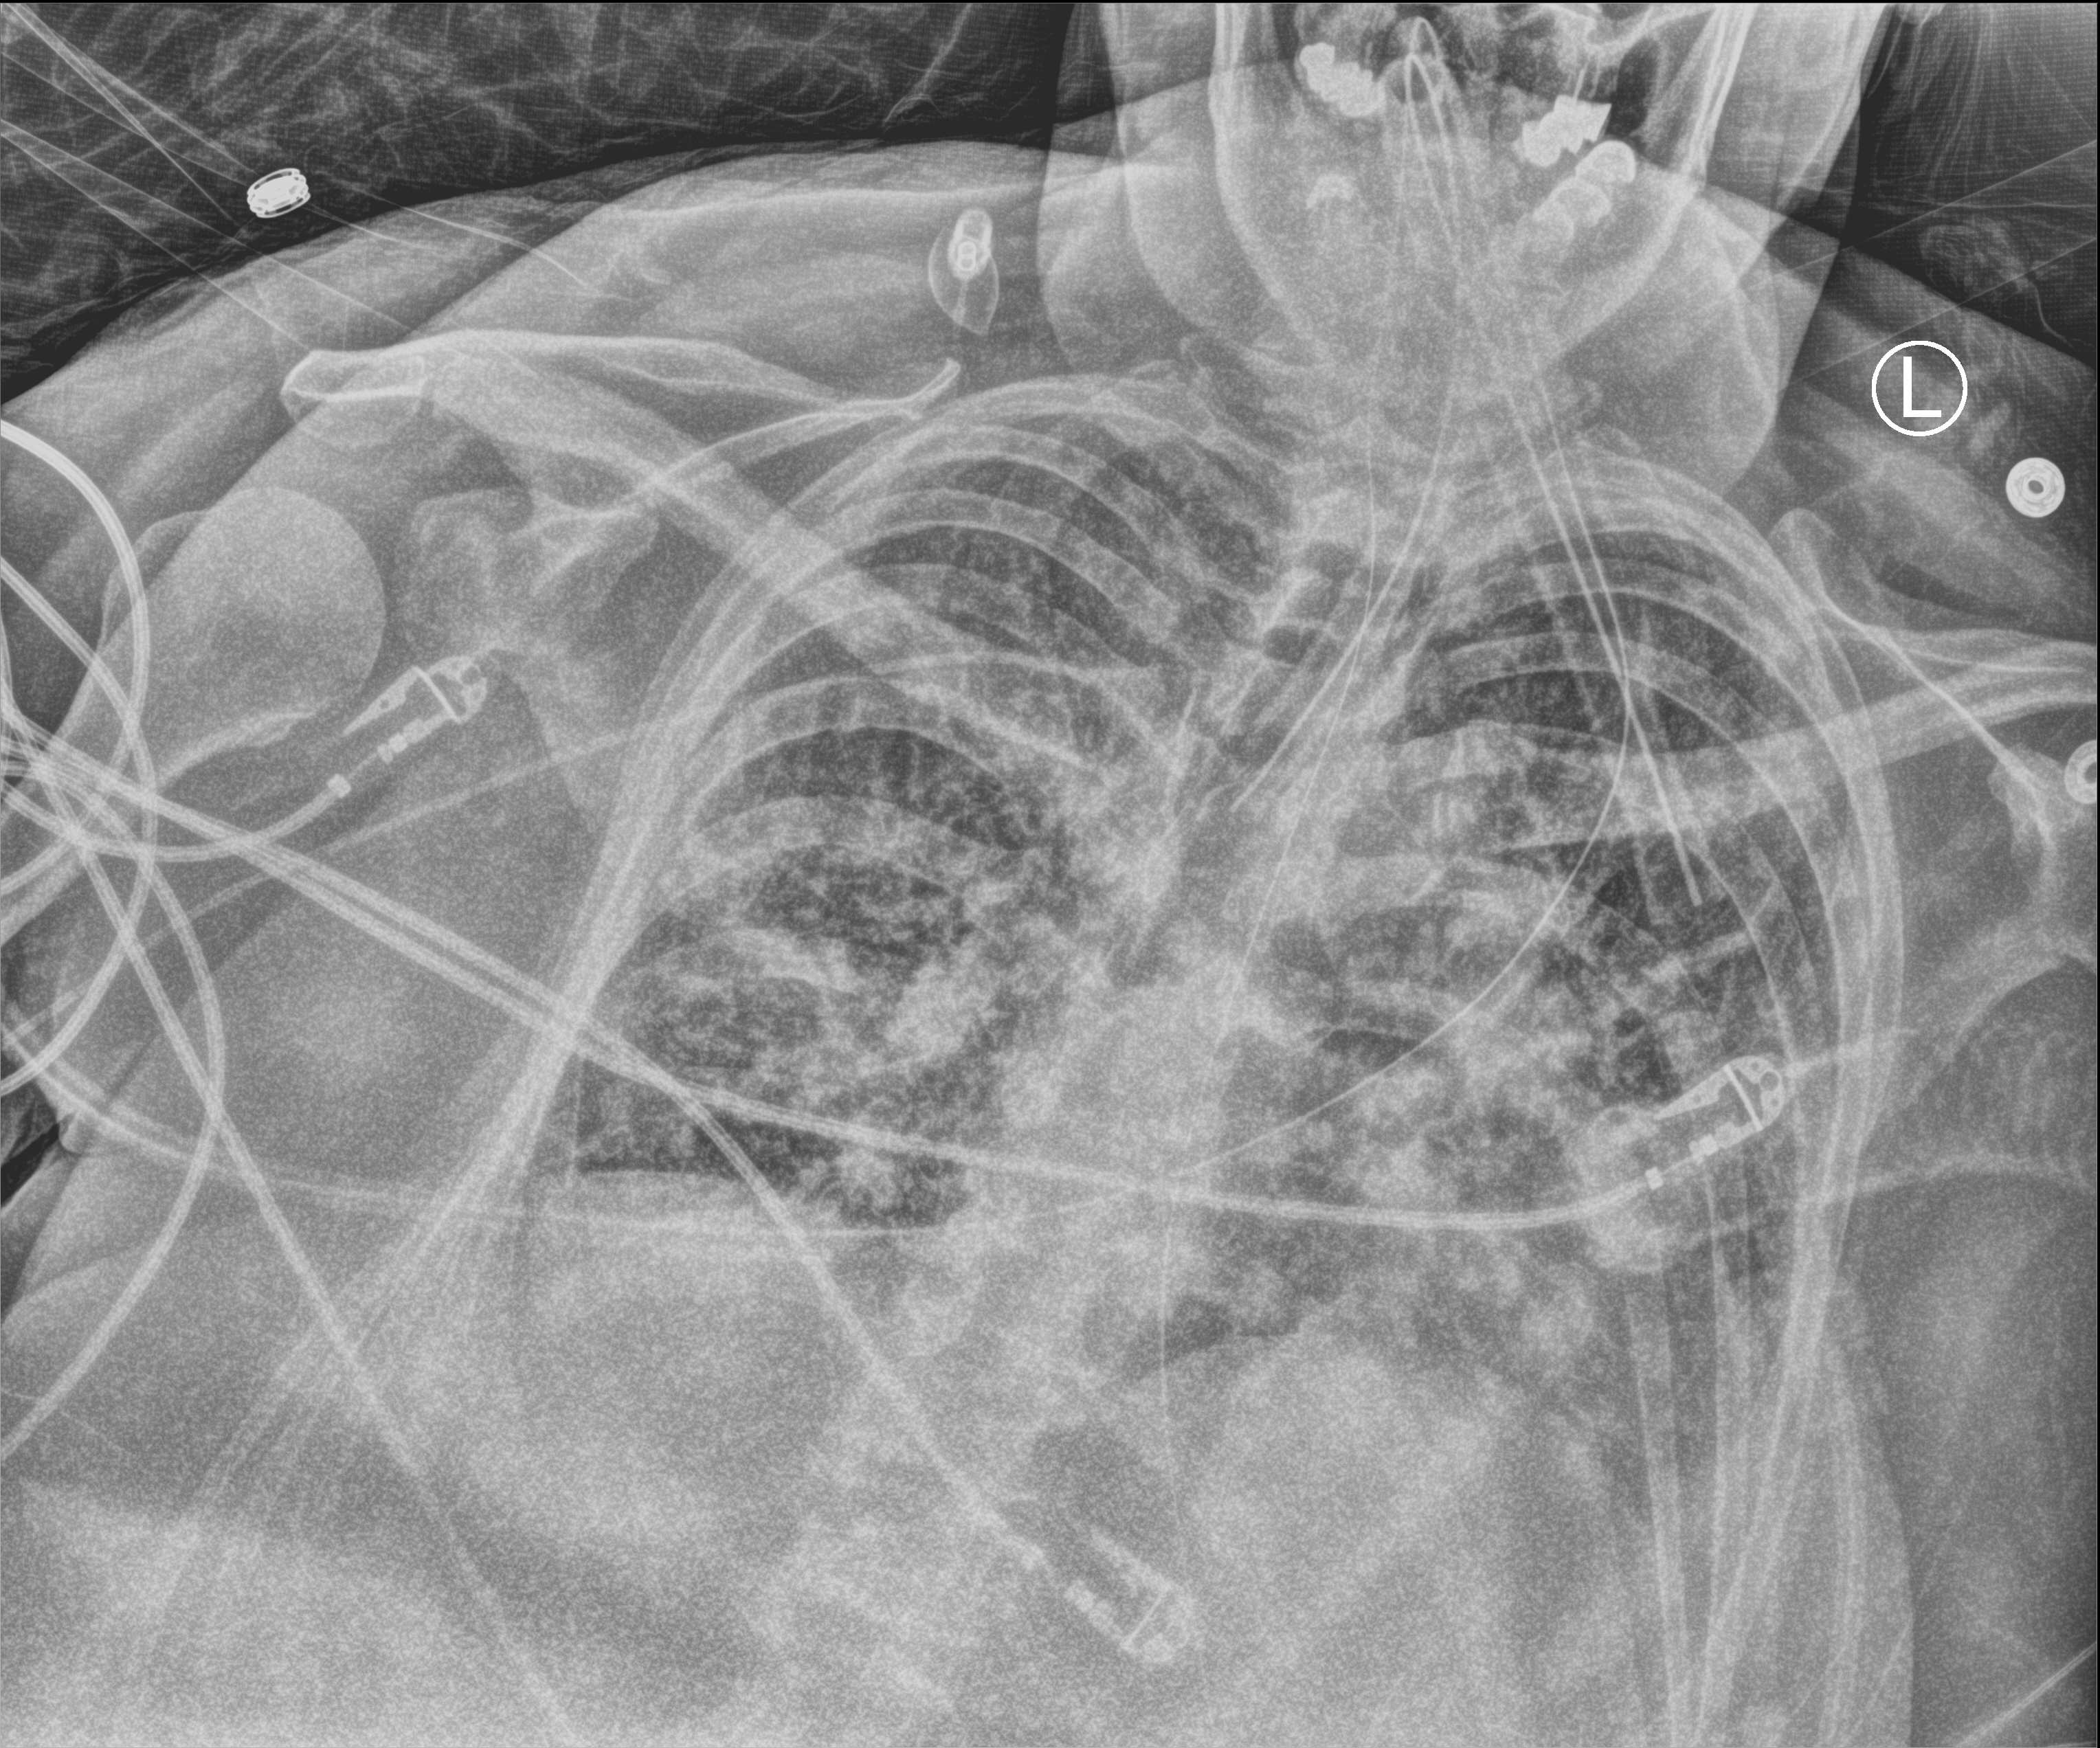
Chest X-ray (portable), anteroposterior (AP) projection. Patient hospitalised with COVID-19; female, aged 60–74 years.
Admission-level facts for this patient (not findings on this image; timing relative to this image not recorded): other chronic lung disease (admission record): yes; admitted to intensive care during this hospital stay: yes.